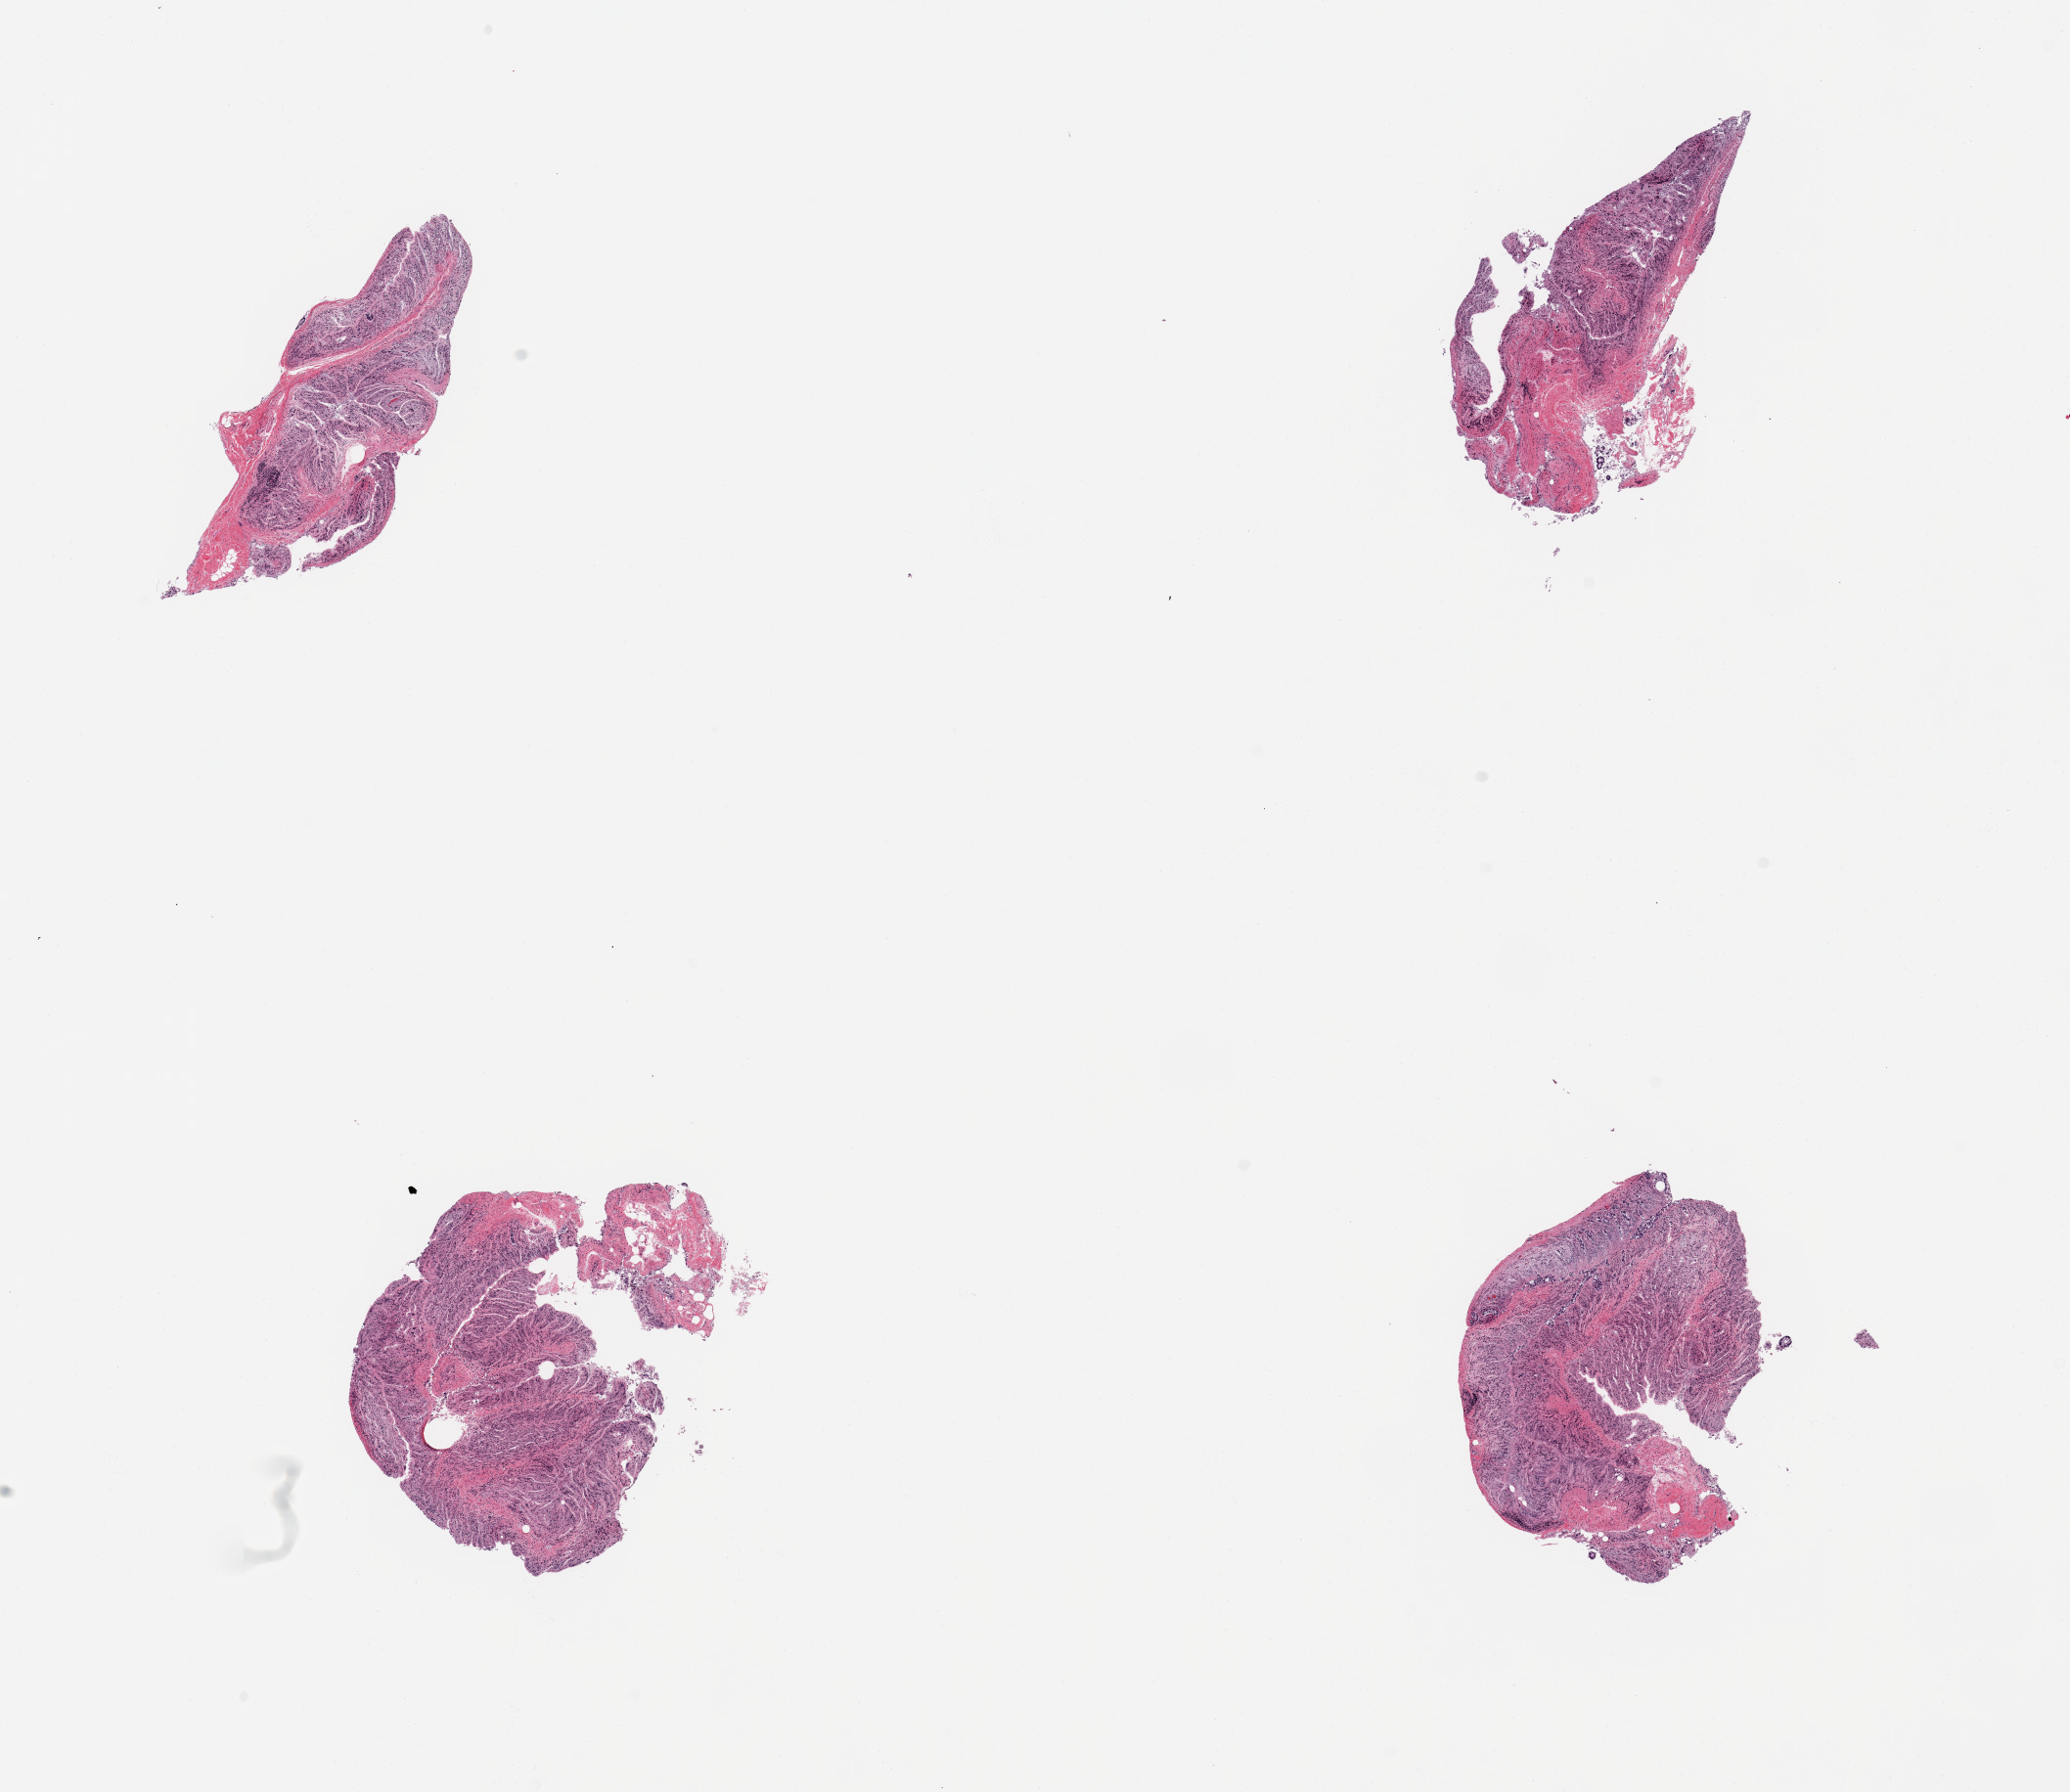
Whole-slide image, hematoxylin and eosin (H&E) stain, shown as a low-resolution overview of the whole scanned area (about 16.7 x 14.5 mm); PAXgene-fixed paraffin-embedded (PFPE) section; section of ileum (target tissue); donor tissue sample. Female donor.
Pathologist's review note for this sample: 4 pieces; autolyzed mucosa, no significant lymphoid tissue.